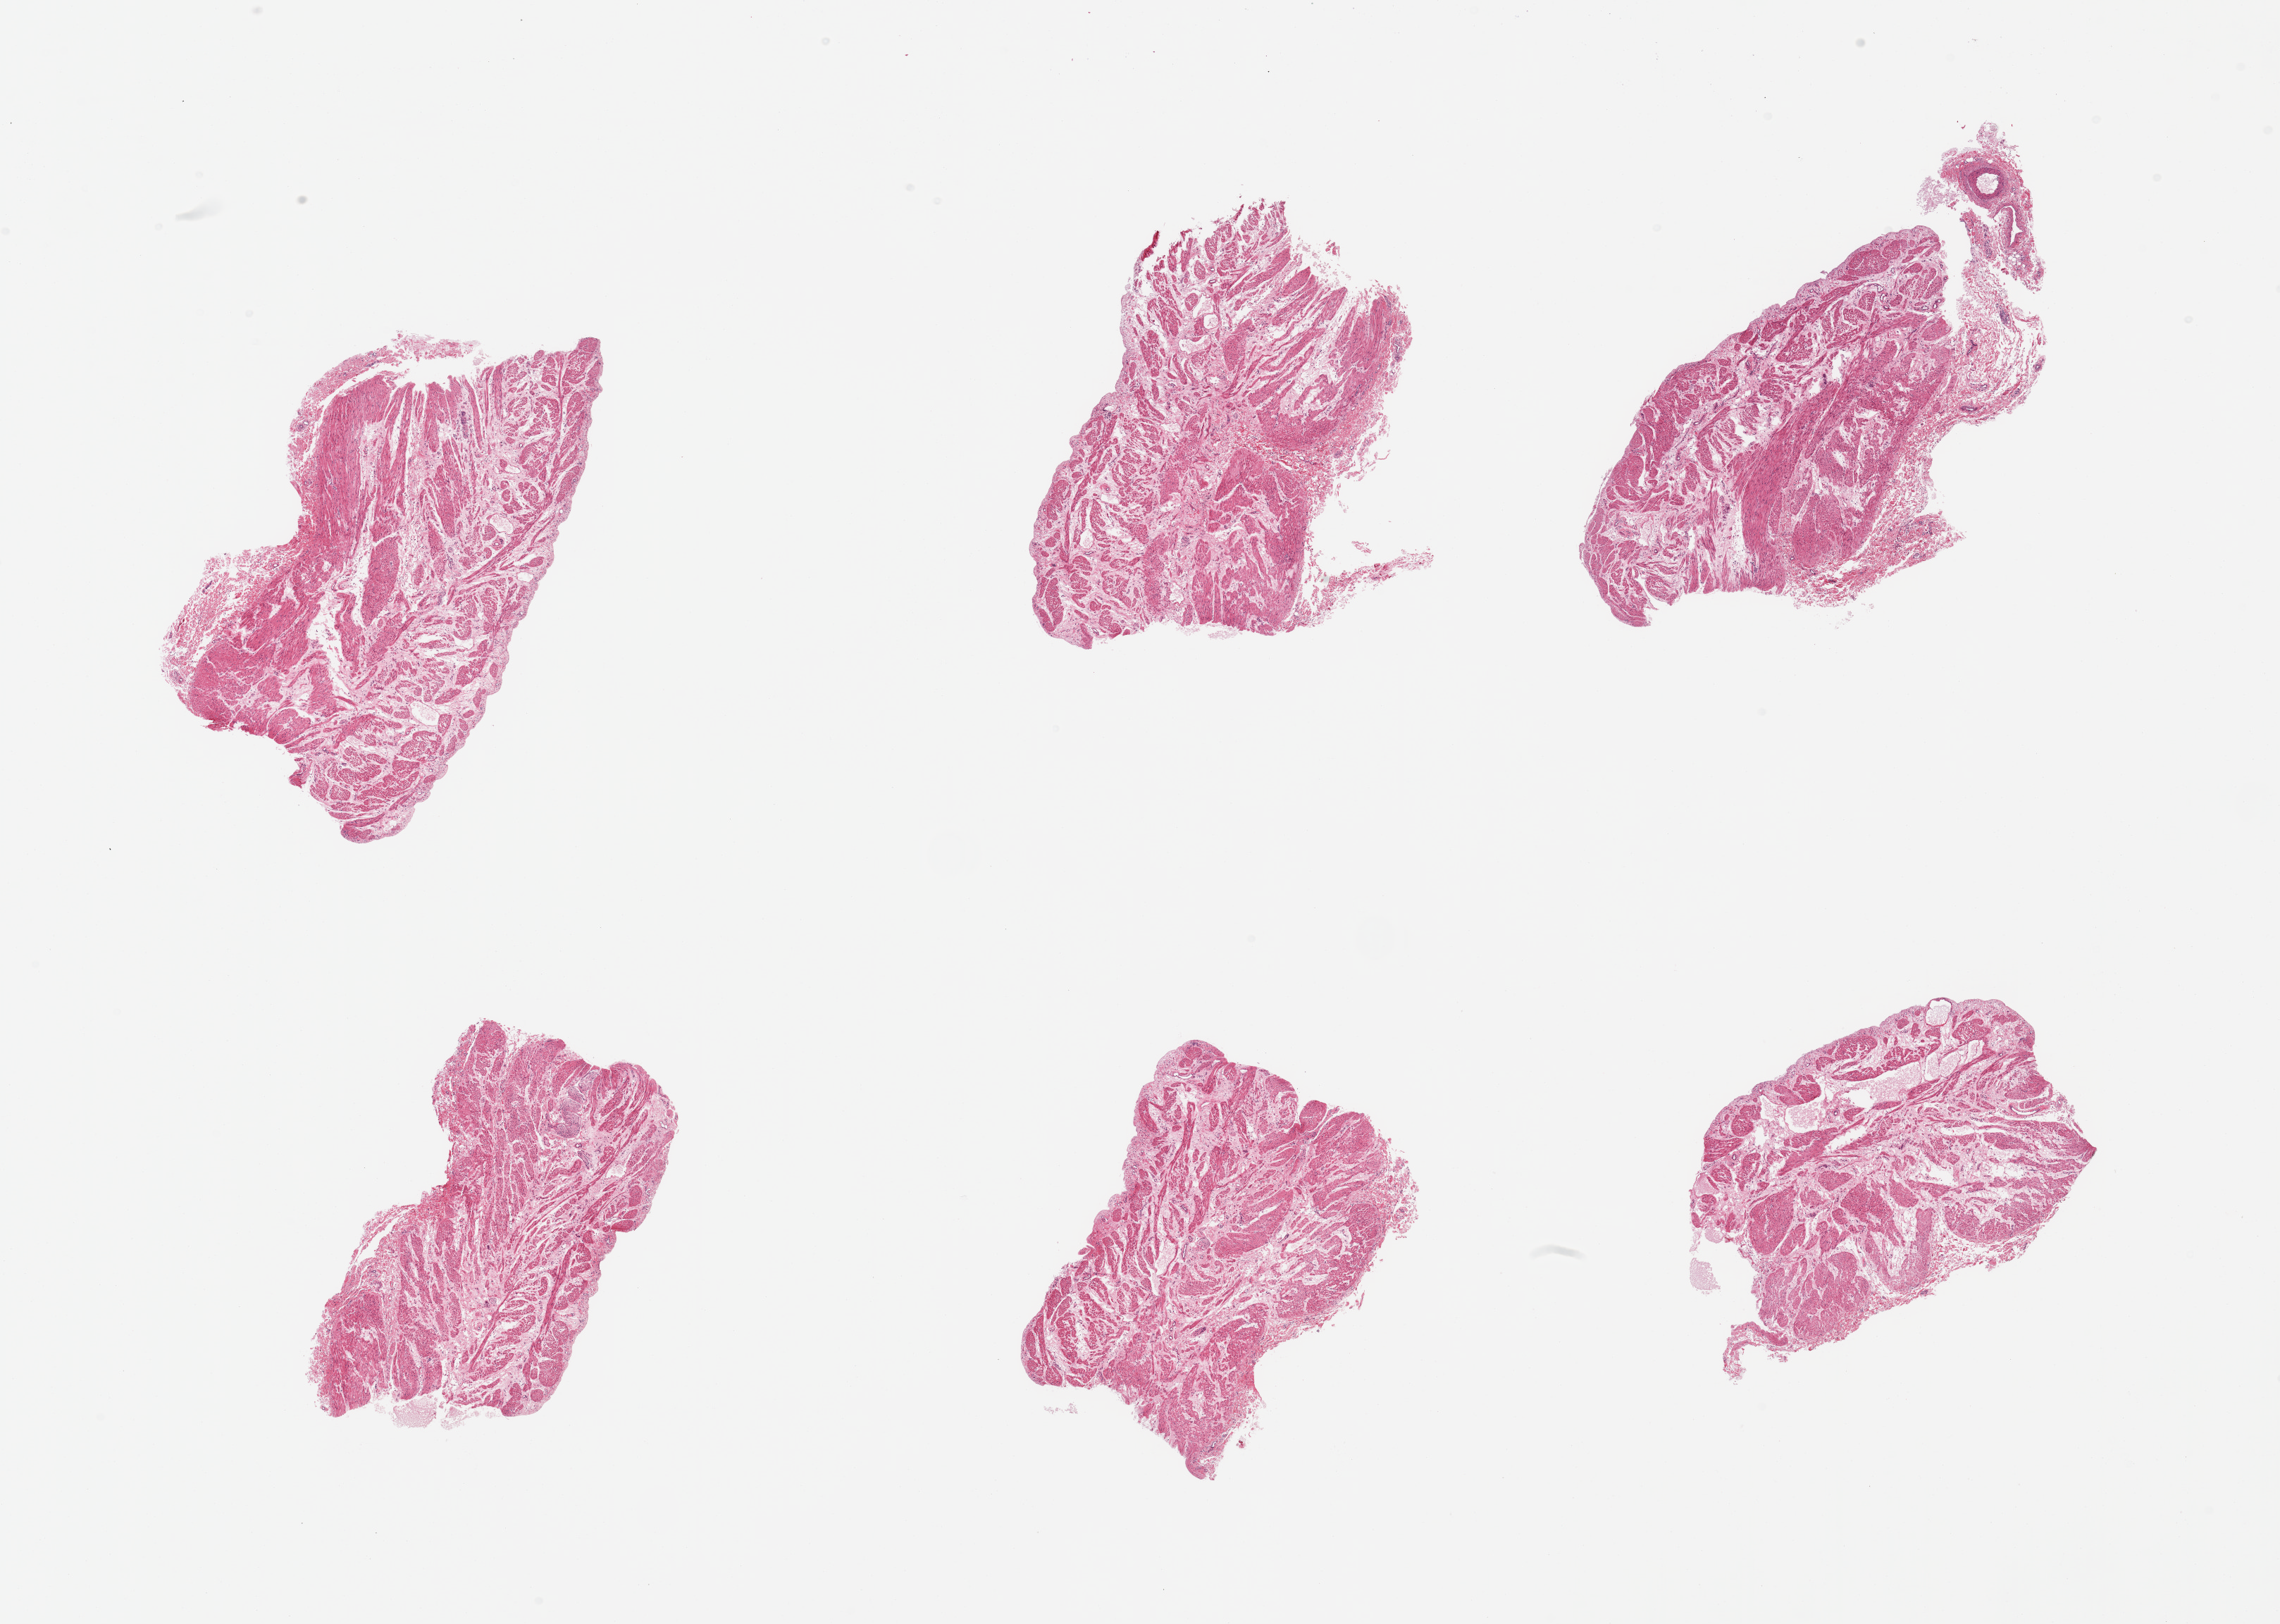
Whole-slide image, hematoxylin and eosin (H&E) stain — low-resolution overview of the scanned area, about 25.6 x 18.2 mm; PAXgene-fixed, paraffin-embedded tissue; section of stomach (target tissue); donor tissue sample. Donor: male.
- pathologist's review note for this sample: 6 pieces; edematous muscularis without mucosa